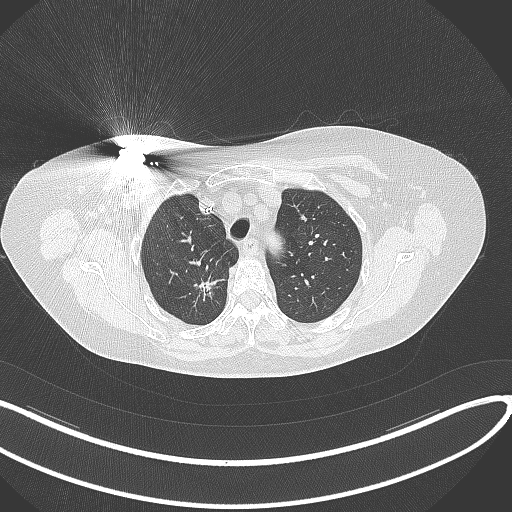
Chest CT, one axial slice; slice 267 of 316 in the series (ordered by position); reconstruction kernel B70f; lung window (W 1500 / L -600 HU); 512 × 512 image matrix, field of view 400 × 400 mm. Female patient, age 72 years. Case-level facts recorded for this patient, not image findings: clinical TNM (as recorded): T1c N0 M0.
Annotated regions visible in this slice (bounding box drawn by a radiologist):
- lung tumour (recorded histology: adenocarcinoma): bounding box [x1, y1, x2, y2] px = [187, 271, 226, 307]